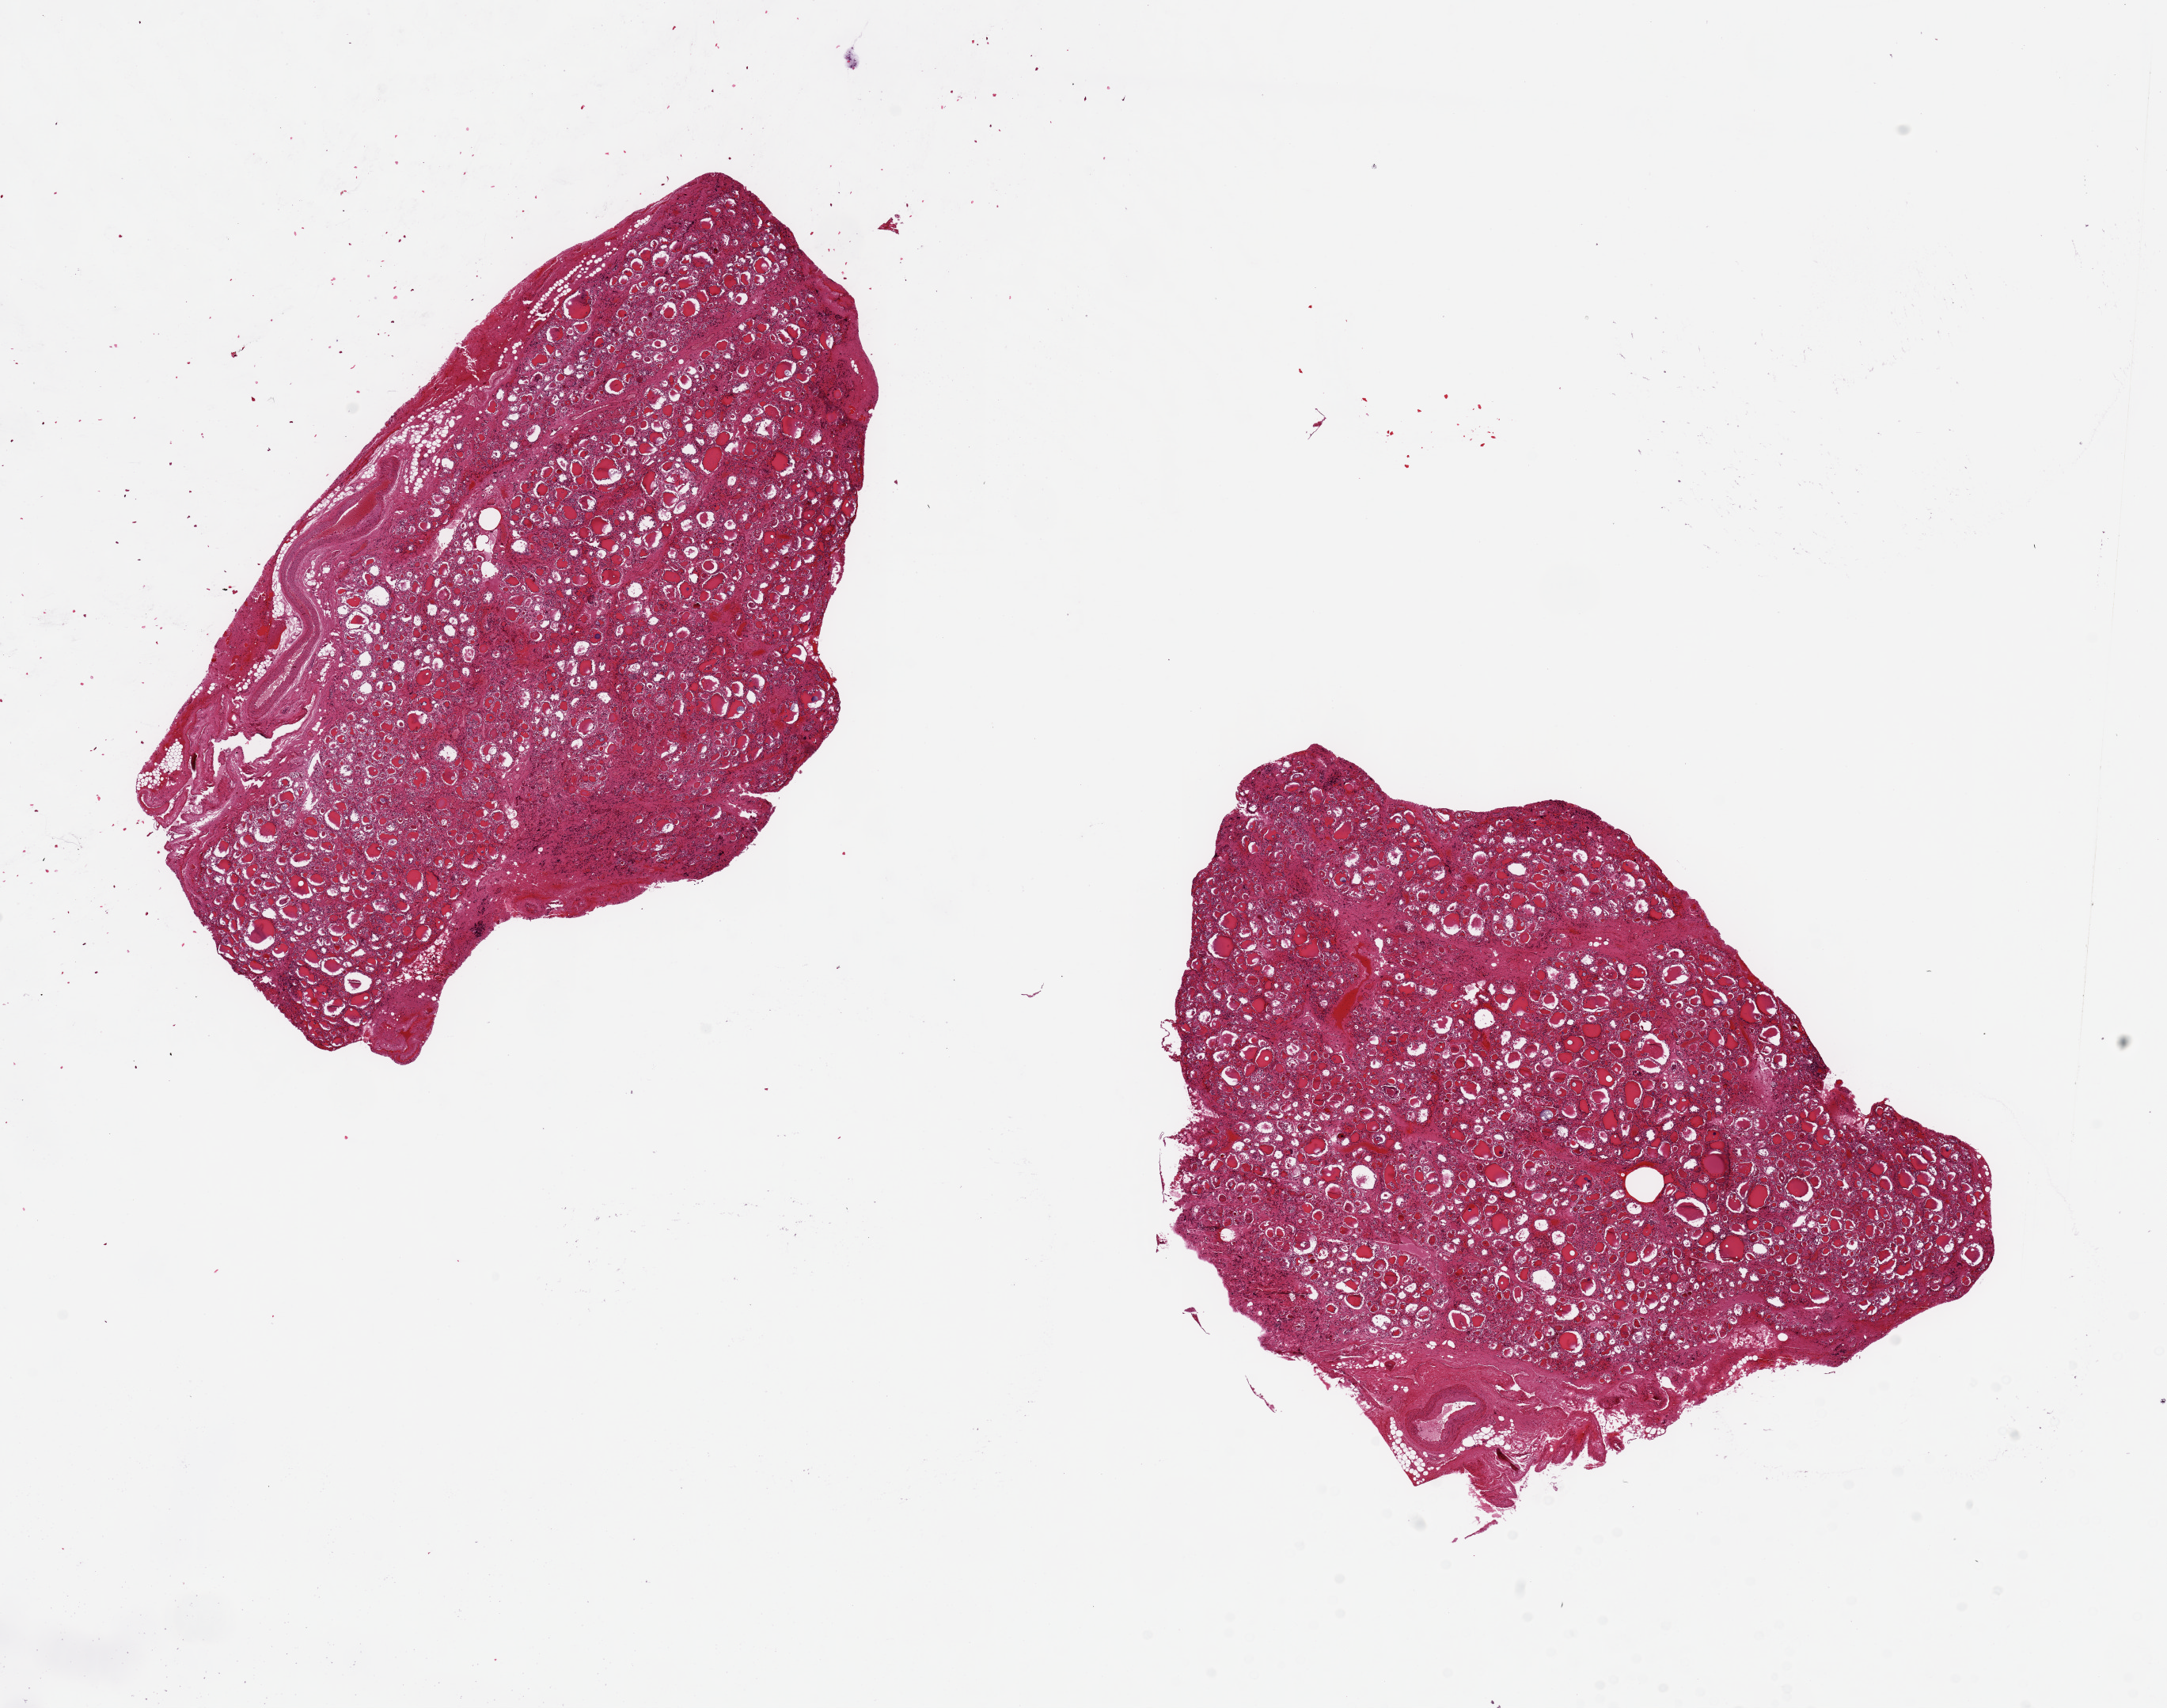
Whole-slide image, hematoxylin and eosin (H&E) stain, a low-resolution overview of the entire scanned area, about 21.7 x 17.1 mm (slide scanned at 20x), PAXgene-fixed, paraffin-embedded tissue, section of thyroid (target tissue), tissue donor sample.
Pathologist's review note for this sample: 2 pieces ~9x5mm.